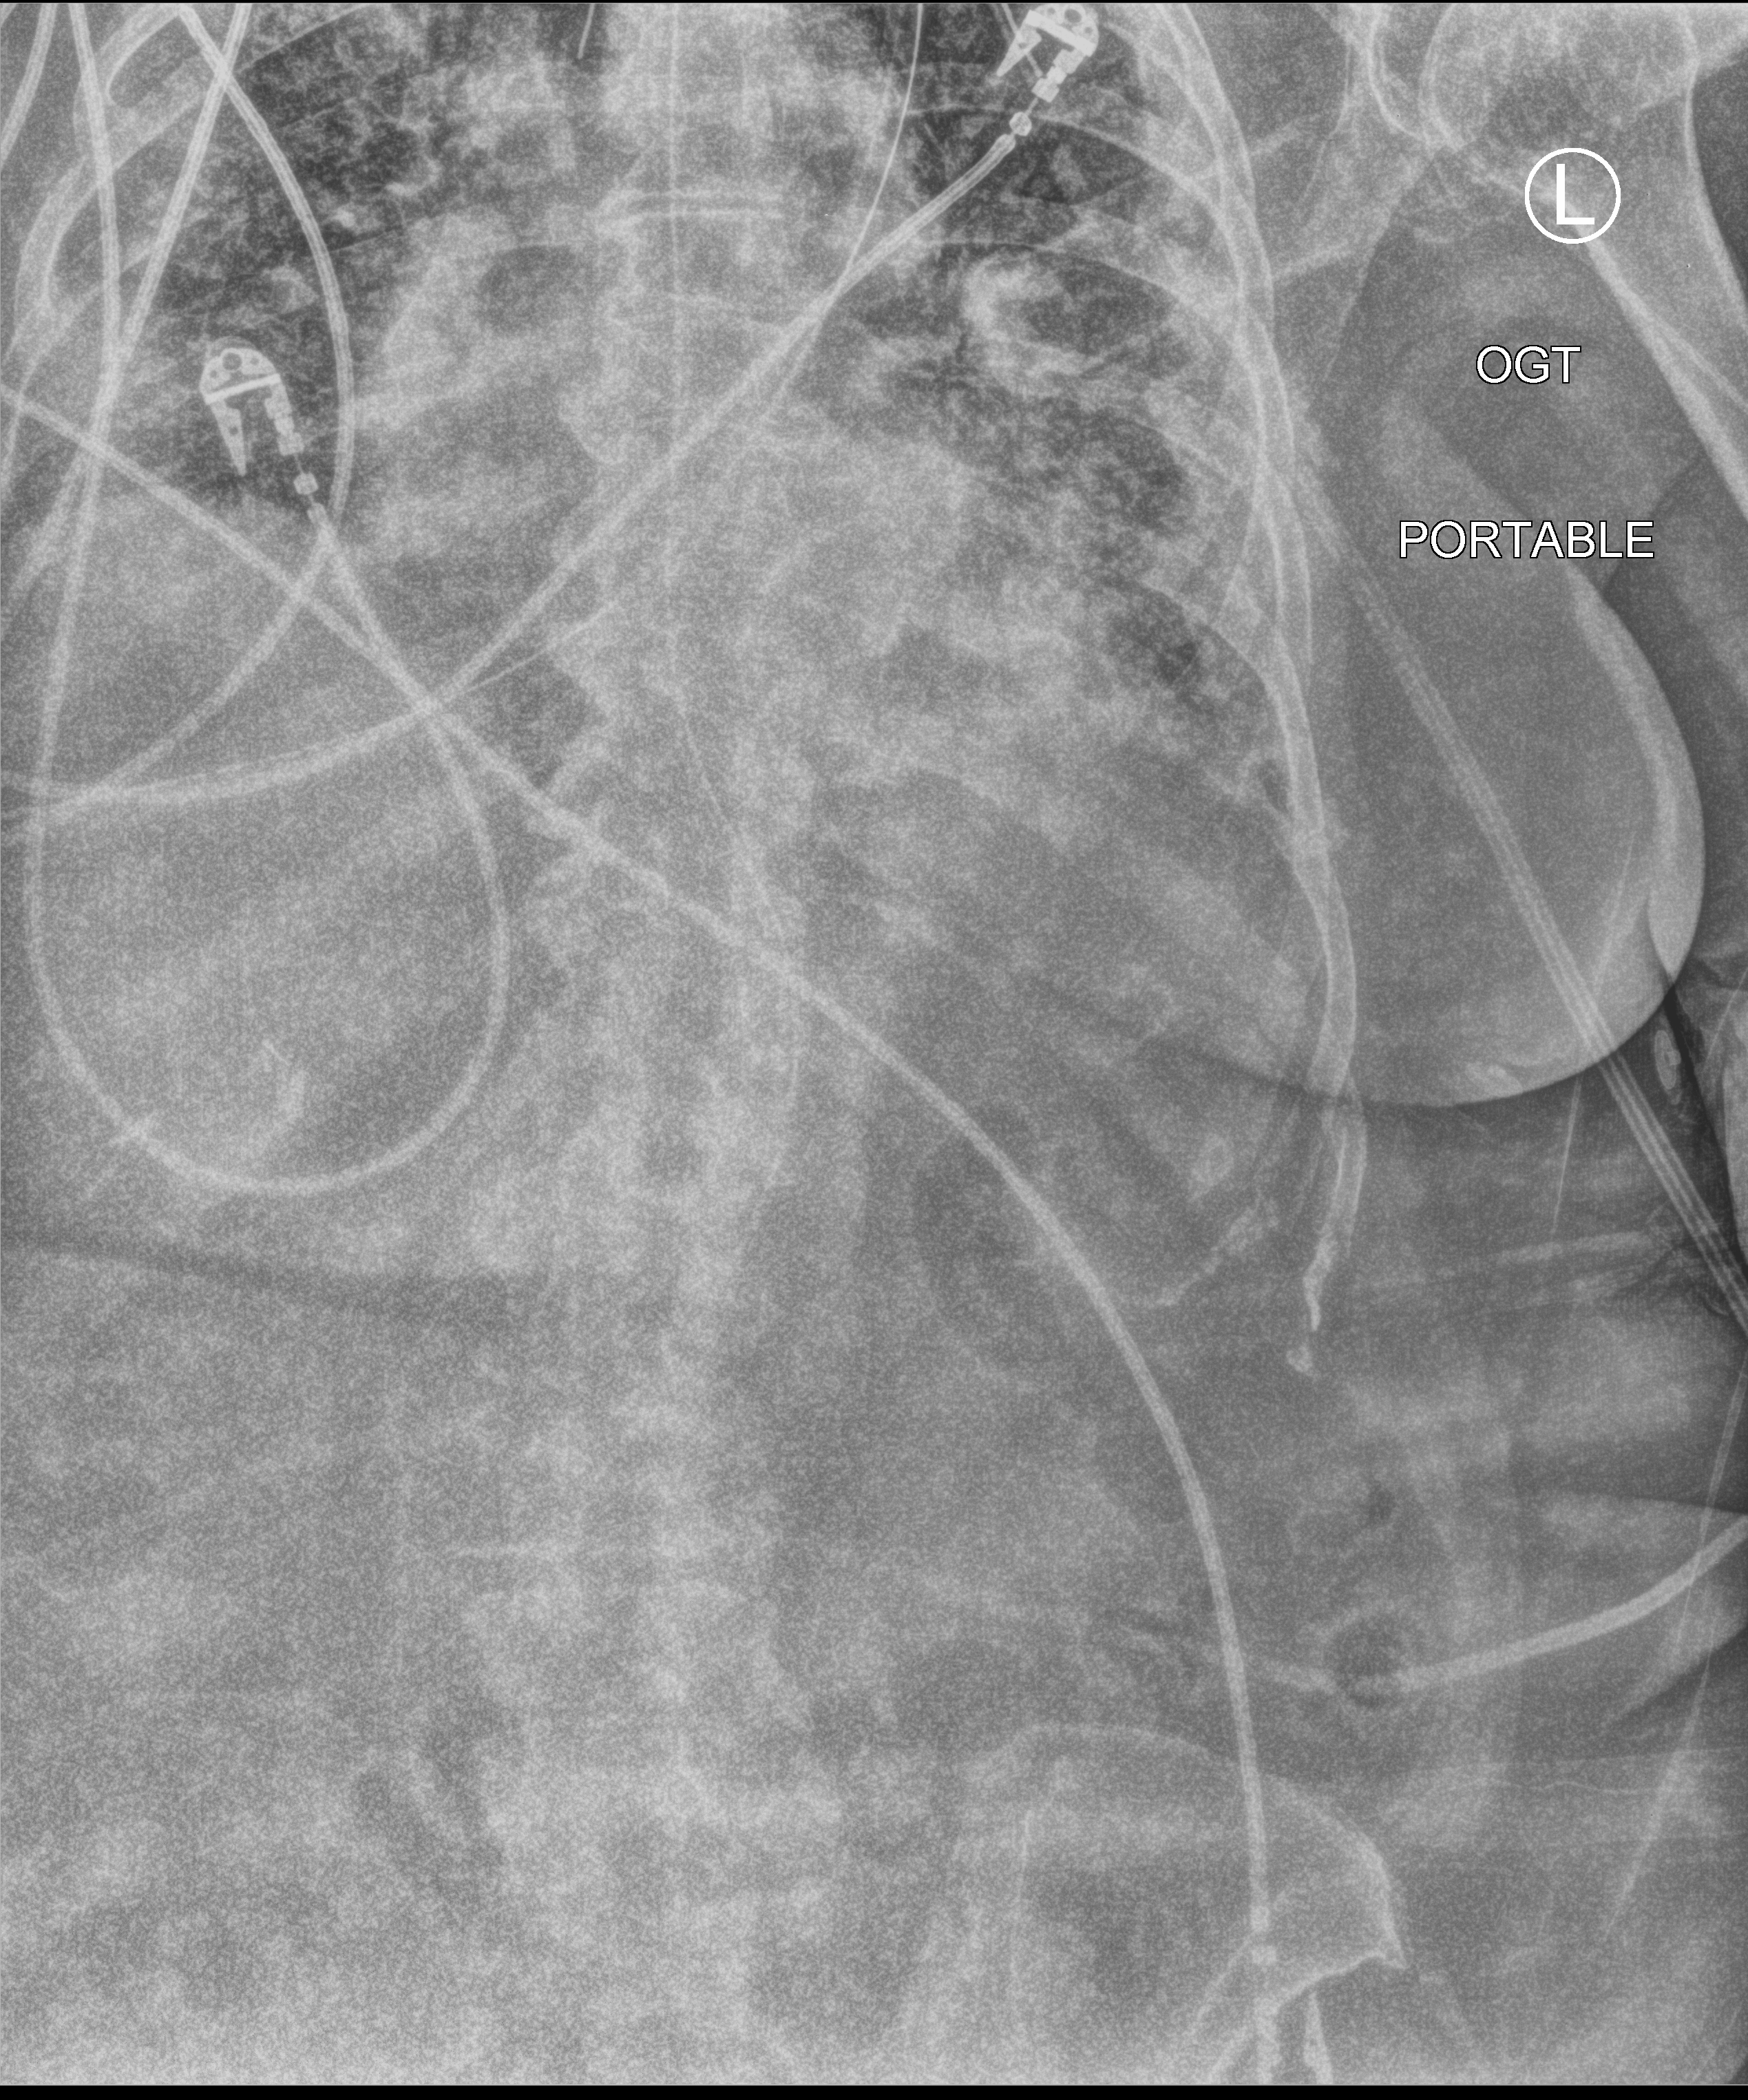
Portable chest radiograph. Female patient hospitalised with COVID-19, age 75–90 years.
Admission-level facts for this patient (not findings on this image; timing relative to this image not recorded):
- length of hospital stay: 56 days